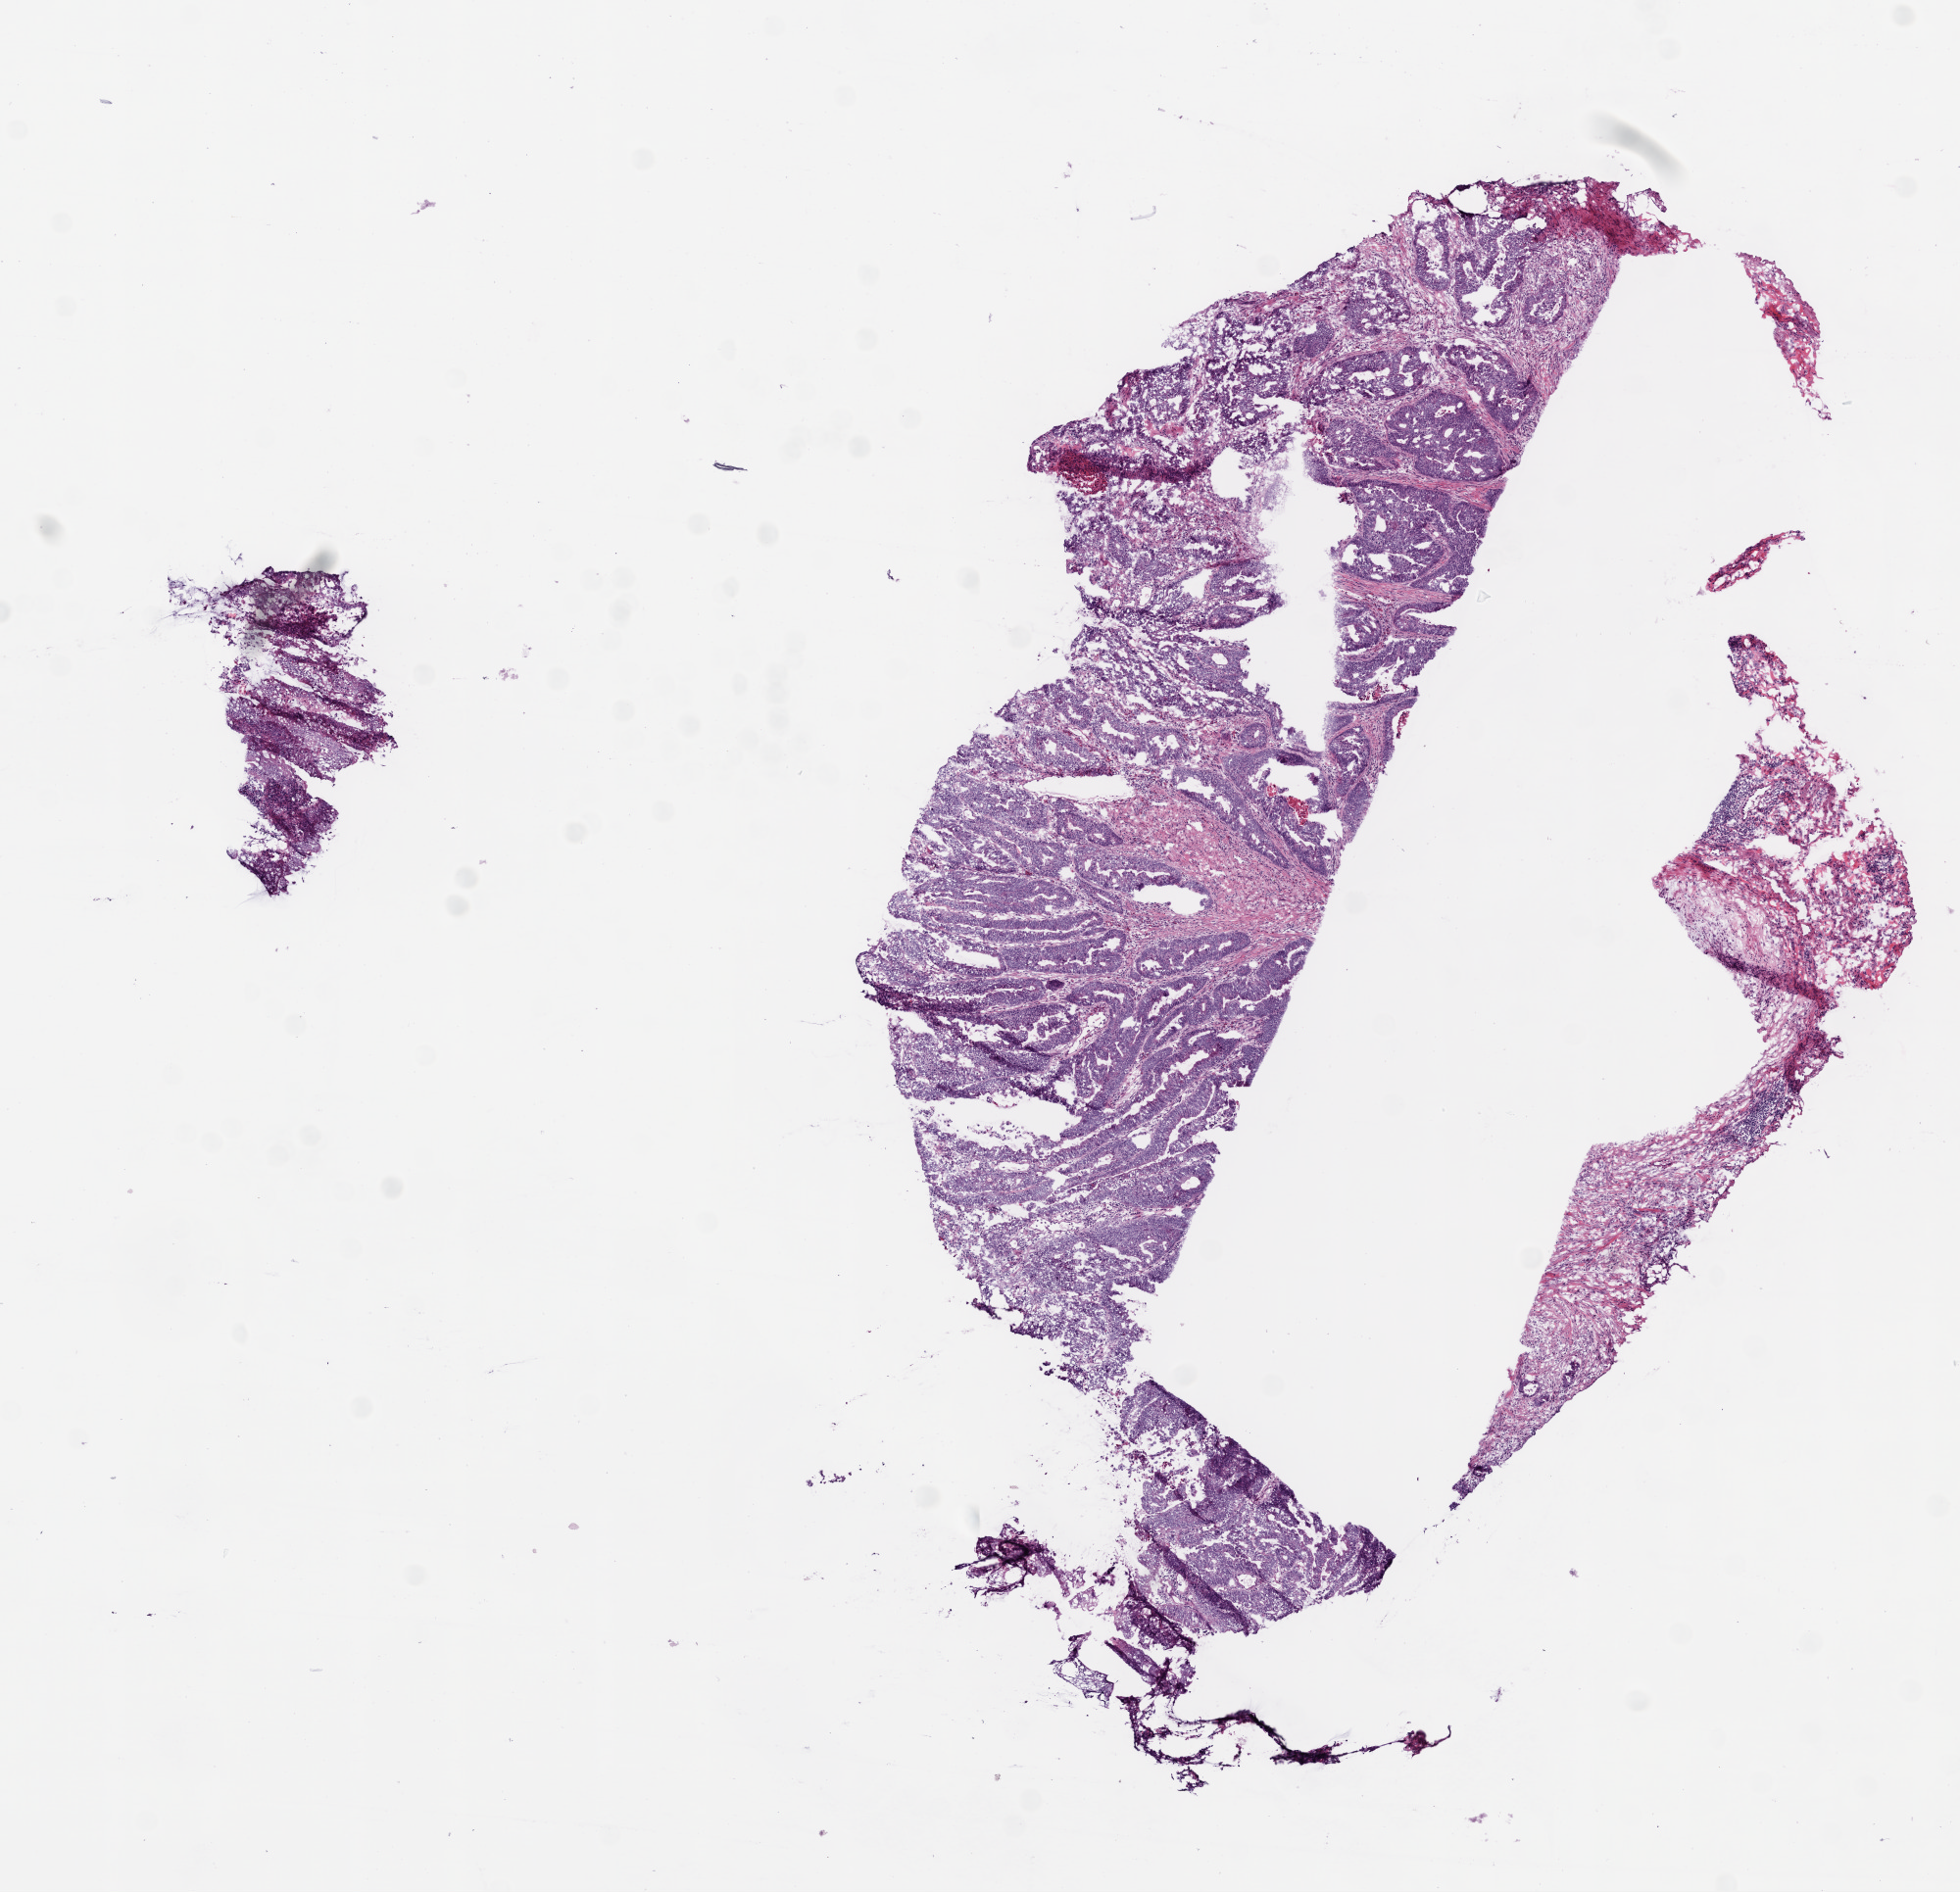
Digitized H&E tissue section (whole slide) — a low-resolution overview of the entire scanned area, about 8.0 x 7.7 mm (slide scanned at 20x), frozen section, primary tumour sample from the colon. Male, age 65 years at initial diagnosis. Pathologist review of this section (percent, as recorded): tumour cells 79%, tumour nuclei 80%, normal cells 0%, stromal cells 20%, necrosis 1%.
Pathologic diagnosis: Adenocarcinoma, NOS (cecum). Lymph nodes positive (case pathology): 0 of 36 examined. AJCC pathologic stage: IIA (6th edition). TNM: T3 N0 M0.